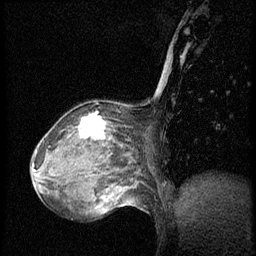
Breast MRI (dynamic contrast-enhanced), one sagittal slice; slice 22 of 56 in the series (ordered by position); dynamic contrast-enhanced series, image 2 of 3 at this slice position (ordered by acquisition); 1.5 T; TE 4.2 ms, TR 20.4 ms; 2 mm slice thickness; 256 × 256 image matrix. Female patient, age 64 years. From the clinical record (not read from this slice): setting: breast cancer imaged before/during neoadjuvant chemotherapy; receptor status: HR-positive, HER2-negative.
Outlined on this slice (semi-automatic segmentation, software-assisted and operator-edited):
- analysis volume of interest (the breast-tissue region the enhancement analysis was run in; not a lesion): box from (x=48, y=101) to (x=142, y=186) px
- tumour enhancement mask (voxels above the 70 % enhancement threshold inside the analysis volume of interest): (x=79, y=114)–(x=106, y=139)